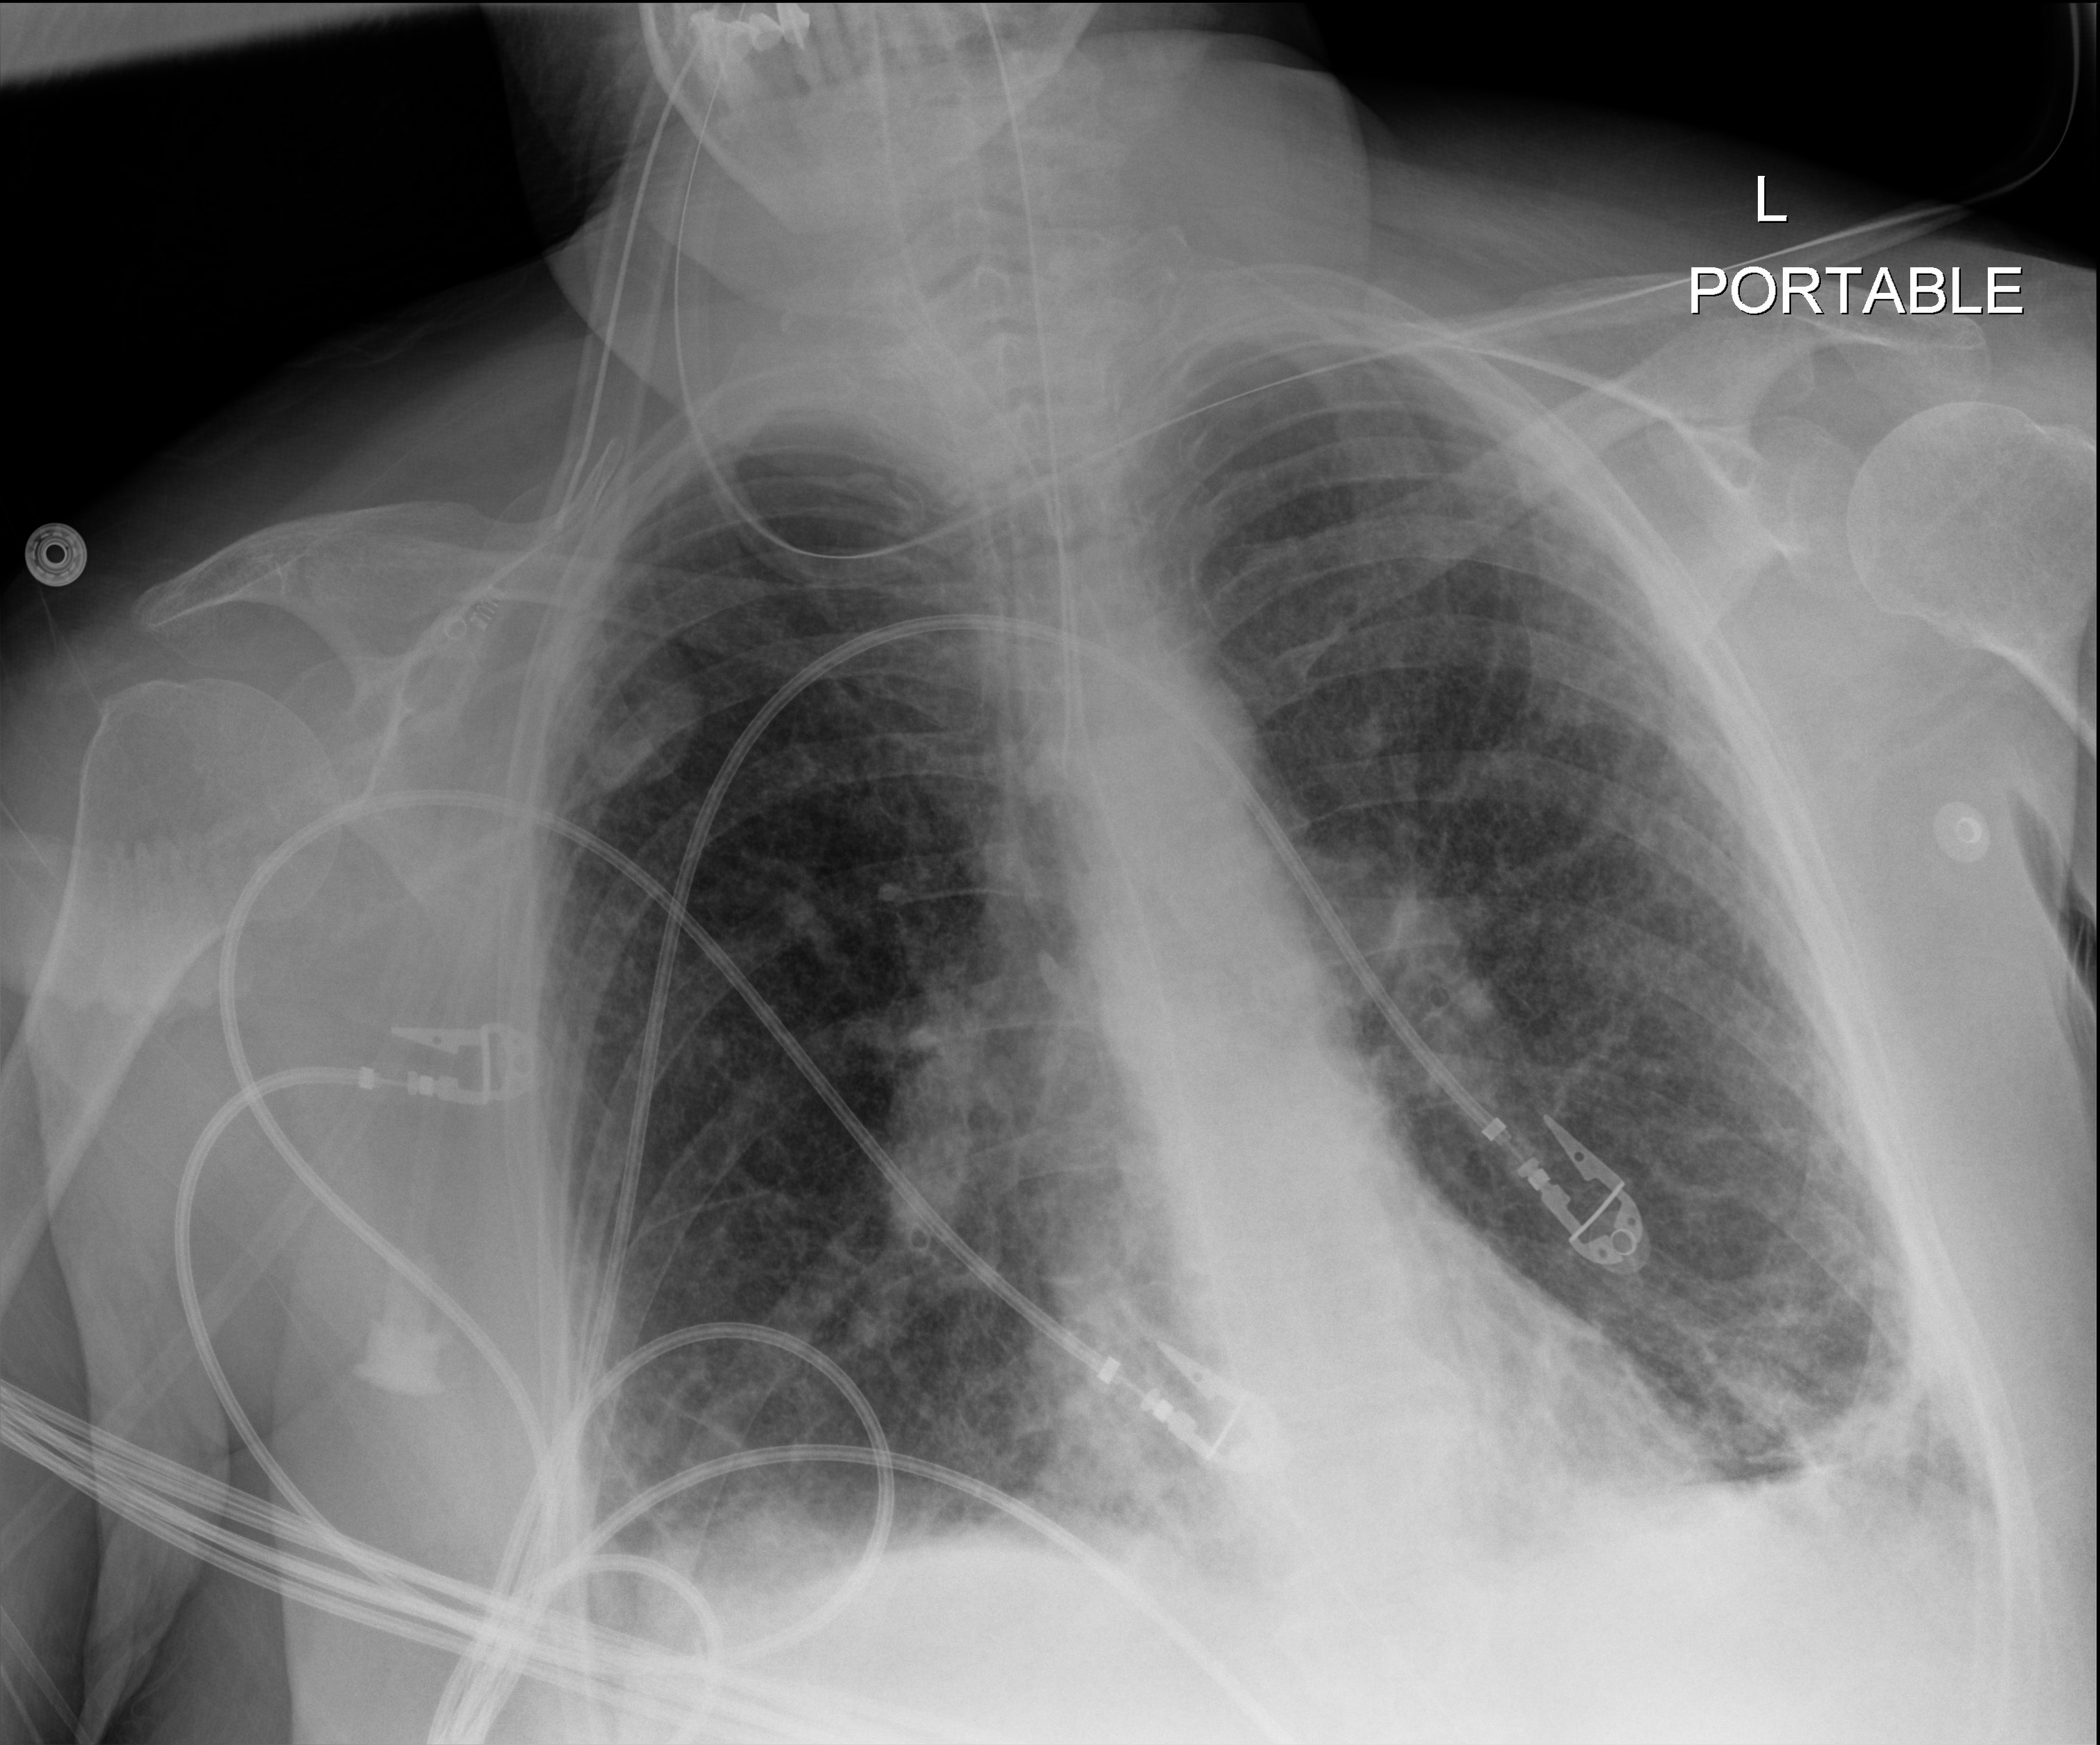
Bedside chest radiograph (digital radiography), anteroposterior (AP) projection. Patient hospitalised with COVID-19; female, aged 60–74 years.
From the hospital-stay record, not from the radiograph (when in the stay this image was taken is not recorded):
- length of hospital stay: 19 days
- smoking status (admission record): former